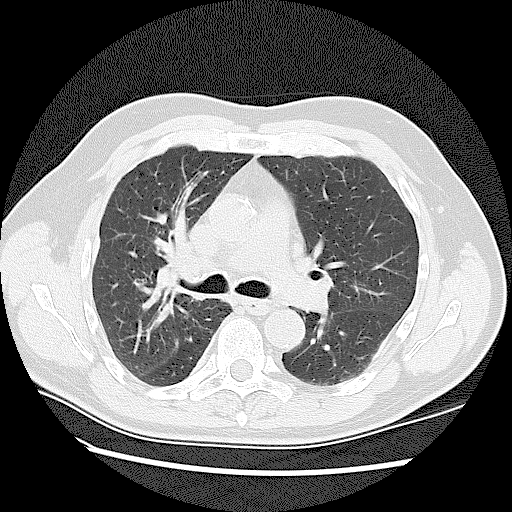
Low-dose screening chest CT, axial slice. First (baseline) screen. Lung window (W 1500 / L -600 HU). Lung (sharp) reconstruction kernel (LUNG). 120 kVp. Slice 51 of 128 in the series. 512 × 512 image matrix. Male, age 72 years at enrolment. Current smoker at enrolment.
Expert reader's lesion annotation, bounding box <133,197,181,237> (left, top, right, bottom; pixels). The screening reader recorded 2 non-calcified nodules or masses ≥4 mm on this exam; which of them this box marks is not recorded. Official screen result: positive, change unspecified: nodule(s) >= 4 mm or enlarging nodule(s), mass(es), or other non-specific abnormalities suspicious for lung cancer. Lung cancer was diagnosed 42 days after this screen: adenocarcinoma, NOS, right upper lobe, stage IV (AJCC 6th edition), 45 mm at pathology.